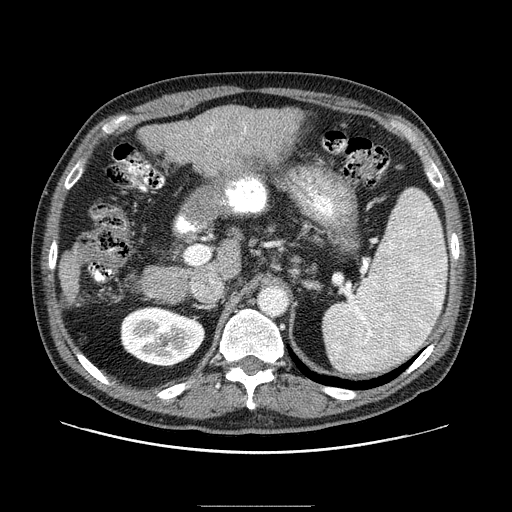
Contrast-enhanced abdominal CT (liver protocol), one axial slice. Slice 47 of 99 in the series (ordered by position). 100 kVp. One of 2 acquisitions stored at this slice position. Soft-tissue window (W 400 / L 40 HU). 2.5 mm slice thickness. 512 × 512 image matrix, field of view 400 × 400 mm. Case-level facts recorded for this patient, not image findings: diagnosis: hepatocellular carcinoma (patient treated with transarterial chemoembolisation; whether this scan precedes or follows treatment is not stated here); TNM stage (as recorded): Stage-II; Child-Pugh class: A; tumour differentiation: well differentiated.
Annotated regions visible in this slice (semi-automatic segmentation, software-assisted and operator-edited):
- liver parenchyma outside the tumour (the mass and vessels are separate outlines, so this box may not span the whole liver): box from (x=59, y=106) to (x=302, y=303) px
- liver vessels: (x=206, y=126)–(x=246, y=133)